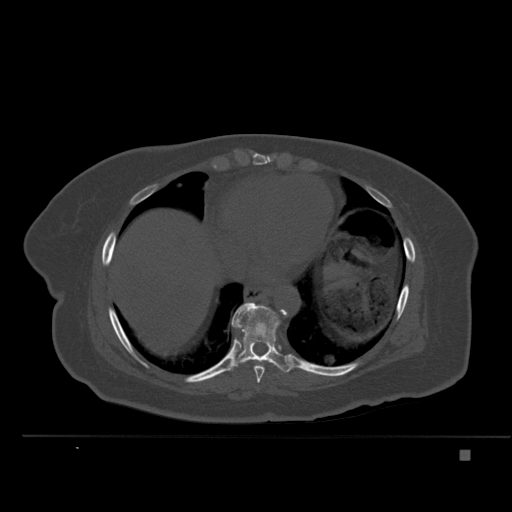
CT including the spine, one axial slice. Position 301 of 477 along the scan axis. Bone window (W 1800 / L 400 HU). 1.5 mm slice thickness. 512 × 512 image matrix. Female patient, age 74 years. Case-level facts recorded for this patient, not image findings: primary cancer: colon.
Annotated regions visible in this slice (semi-automatic segmentation, software-assisted and operator-edited):
- T8 vertebra: bounding box [x1, y1, x2, y2] px = [251, 359, 264, 383]
- T9 vertebra: [228, 302, 296, 373]